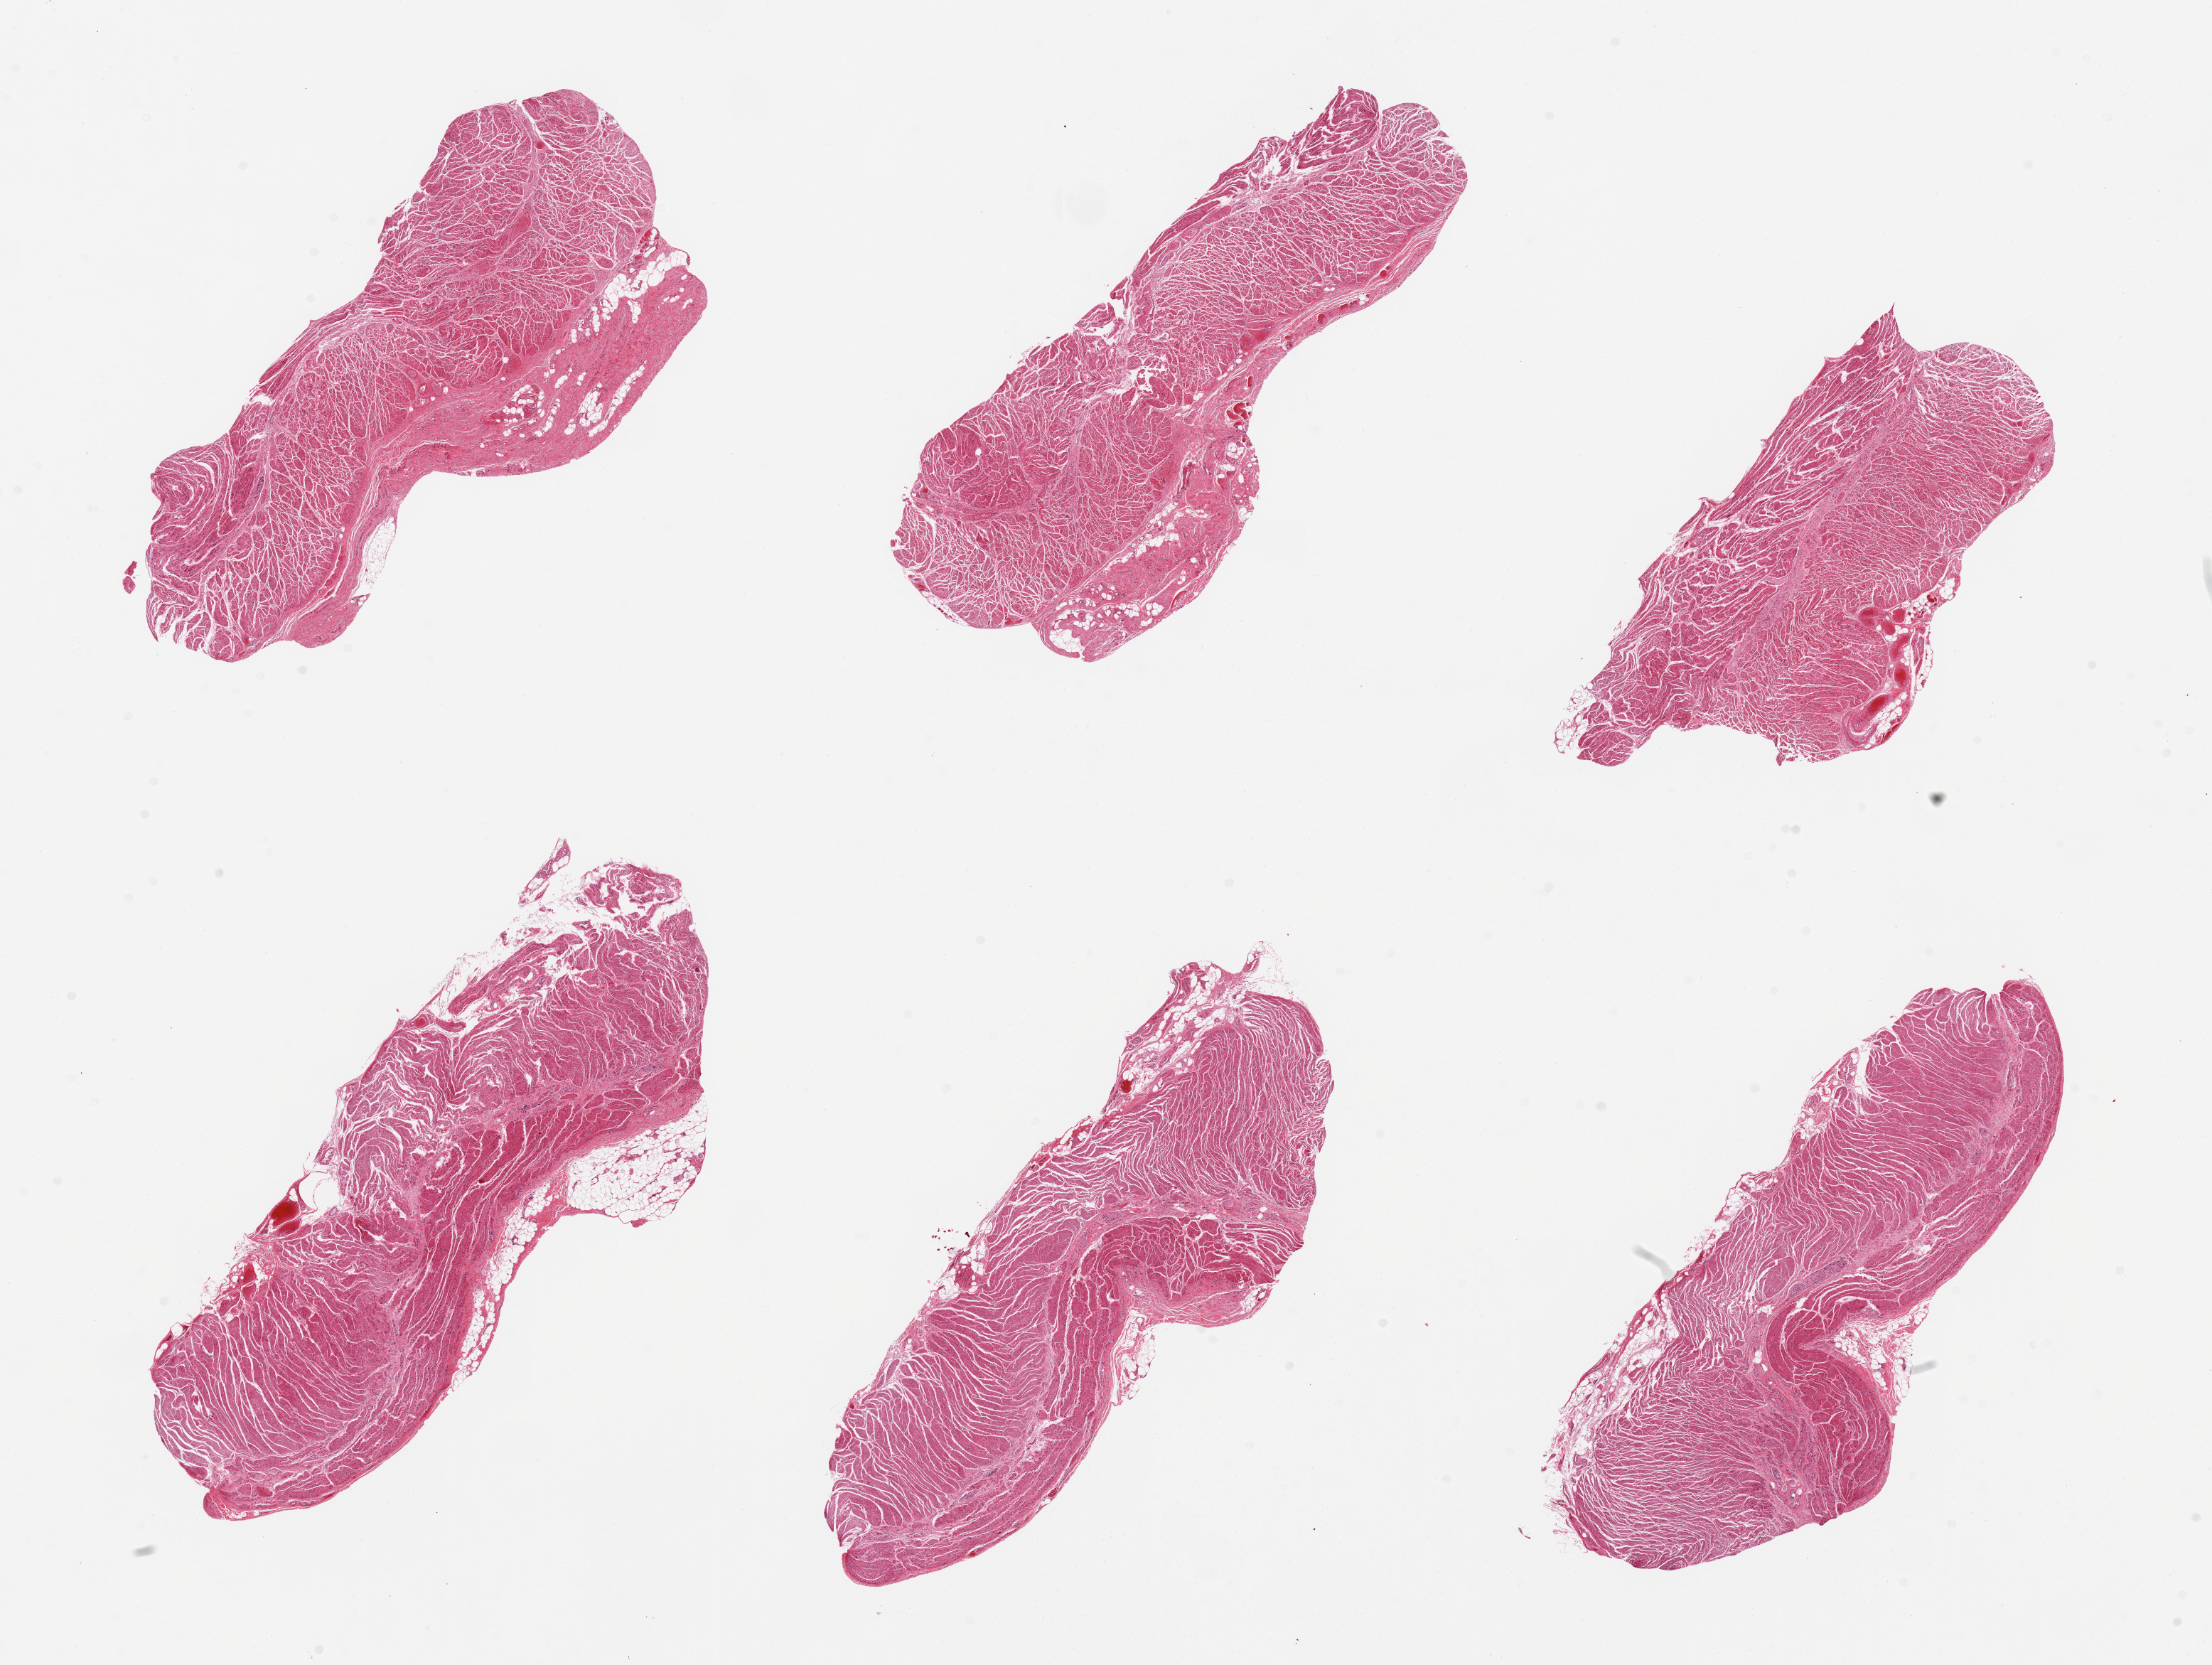
Digitized hematoxylin and eosin (H&E)-stained section, whole scanned area (about 24.6 x 18.5 mm) shown as a low-resolution overview; PAXgene-fixed paraffin-embedded (PFPE) section; target tissue: gastroesophageal junction; donor tissue sample. Donor sex: male.
Review note (as recorded): 6 pieces; prominent (20 & 25%) submucosal fibrous tissue in 2 of 6 pieces.